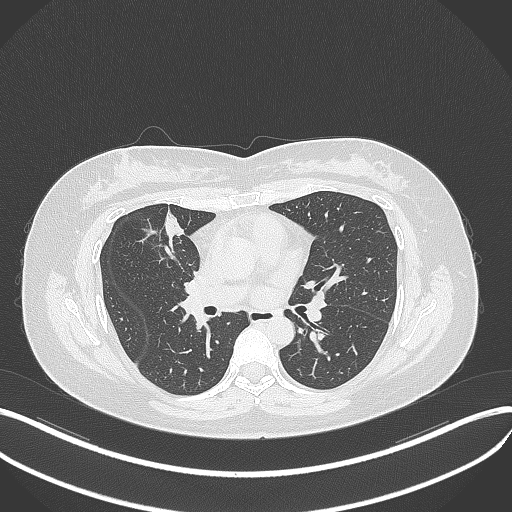
Chest CT, one axial slice. Position 170 of 273 along the scan axis. Lung window (W 1500 / L -600 HU). 1 mm slice thickness. 512 × 512 image matrix, field of view 400 × 400 mm. Patient: female, 42 years. Case-level facts recorded for this patient, not image findings: clinical TNM (as recorded): T1b N0 M0.
Annotated regions visible in this slice (rectangle marked by the reading radiologist):
- lung tumour (recorded histology: adenocarcinoma): bounding box <161,203,190,254> (left, top, right, bottom; pixels)